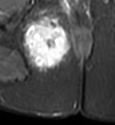
MRI of an extremity soft-tissue mass, one axial slice. Slice 28 of 49 in the series (ordered by position). STIR. MR volume resampled by the dataset authors to the PET/CT grid (not the native acquisition matrix). 3.27 mm slice thickness. 115 × 125 image matrix, field of view 112 × 122 mm. Female patient. From the clinical record (not read from this slice): histological type: epithelioid sarcoma; grade: intermediate; site of the primary tumour: right buttock.
Annotated regions visible in this slice (expert contour drawn on MRI and transferred to this co-registered scan by the dataset authors):
- gross tumour volume including surrounding oedema: bounding box [x1, y1, x2, y2] px = [22, 14, 69, 70]
- gross tumour volume (mass): [26, 23, 62, 65]